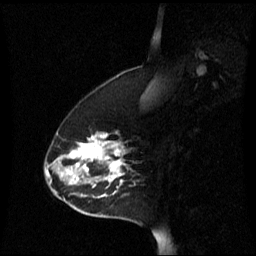
Breast MRI (dynamic contrast-enhanced), one sagittal slice; slice 18 of 60 in the series (ordered by position); dynamic contrast-enhanced series, image 2 of 3 at this slice position (ordered by acquisition); 1.5 T; TE 4.2 ms, TR 8.4 ms; 2.2 mm slice thickness; 256 × 256 image matrix, field of view 240 × 240 mm. Female patient, age 45 years. From the clinical record (not read from this slice): setting: breast cancer imaged before/during neoadjuvant chemotherapy; receptor status: HR-positive, HER2-negative.
Outlined on this slice (semi-automatically segmented with operator editing):
- analysis volume of interest (the breast-tissue region the enhancement analysis was run in; not a lesion): bounding box <44,132,135,221> (left, top, right, bottom; pixels)
- tumour enhancement mask (voxels above the 70 % enhancement threshold inside the analysis volume of interest): <46,134,125,199>